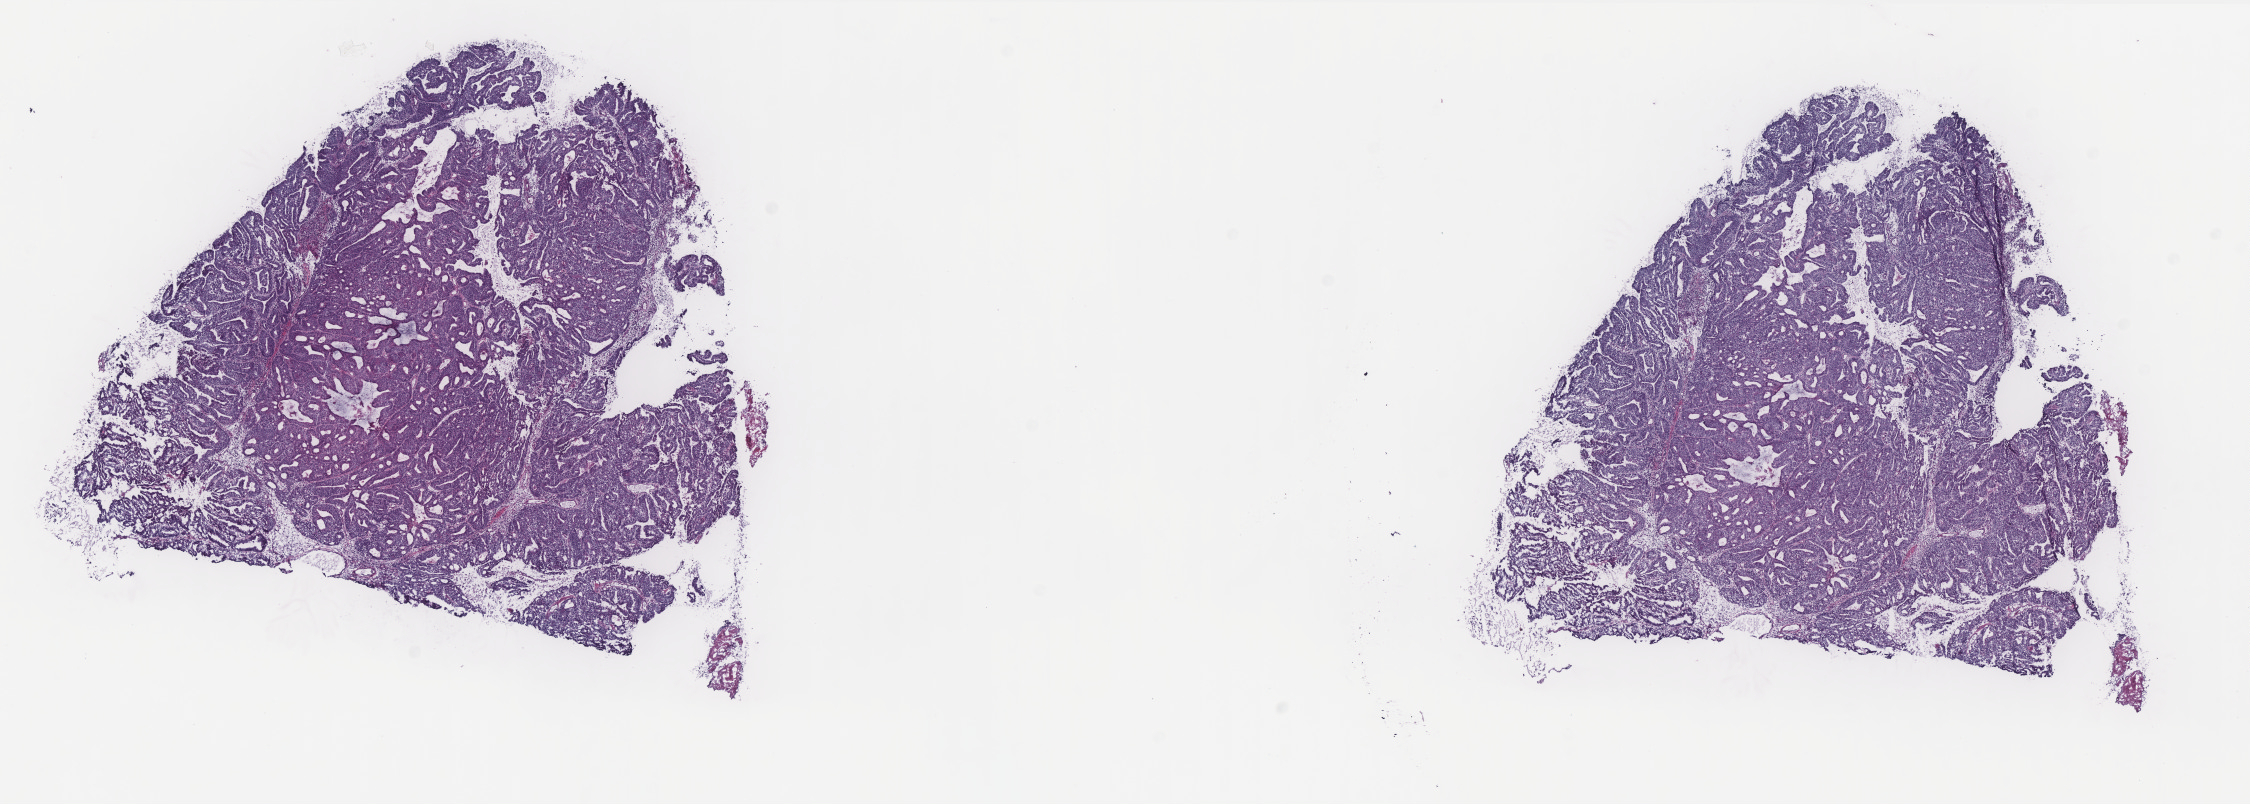
Whole-slide histology image, H&E-stained — low-resolution overview of the scanned area, about 18.0 x 6.4 mm; frozen section from the top of the tissue portion; primary tumour sample from the uterus. Female, age 75 years at initial diagnosis. Histologic grade: G2 (moderately differentiated). Slide review estimates, as recorded: tumour cells 100%, tumour nuclei 80%, normal cells 0%, stromal cells 0%, necrosis 0%. Inflammatory infiltration, as recorded: lymphocyte infiltration 0%, monocyte infiltration 0%, neutrophil infiltration 0%.
FIGO stage: IA. Pathologic diagnosis: Endometrioid adenocarcinoma, NOS (endometrium). Lymph nodes positive (case pathology): 0 of 9 examined.